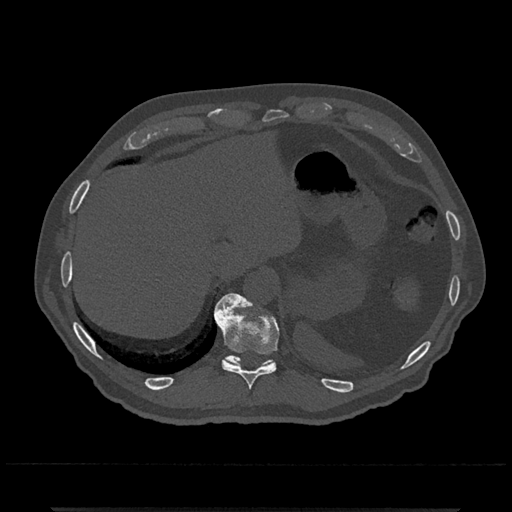
CT including the spine, one axial slice. Reconstruction kernel Br40s/3. Bone window (W 1800 / L 400 HU). 0.5 mm slice thickness. 512 × 512 image matrix. Patient: male, 67 years. Case-level facts recorded for this patient, not image findings: primary cancer: prostate.
Structures marked on this image (semi-automatically segmented with operator editing):
- T10 vertebra: bounding box <214,293,279,390> (left, top, right, bottom; pixels)
- T11 vertebra: <215,297,273,366>